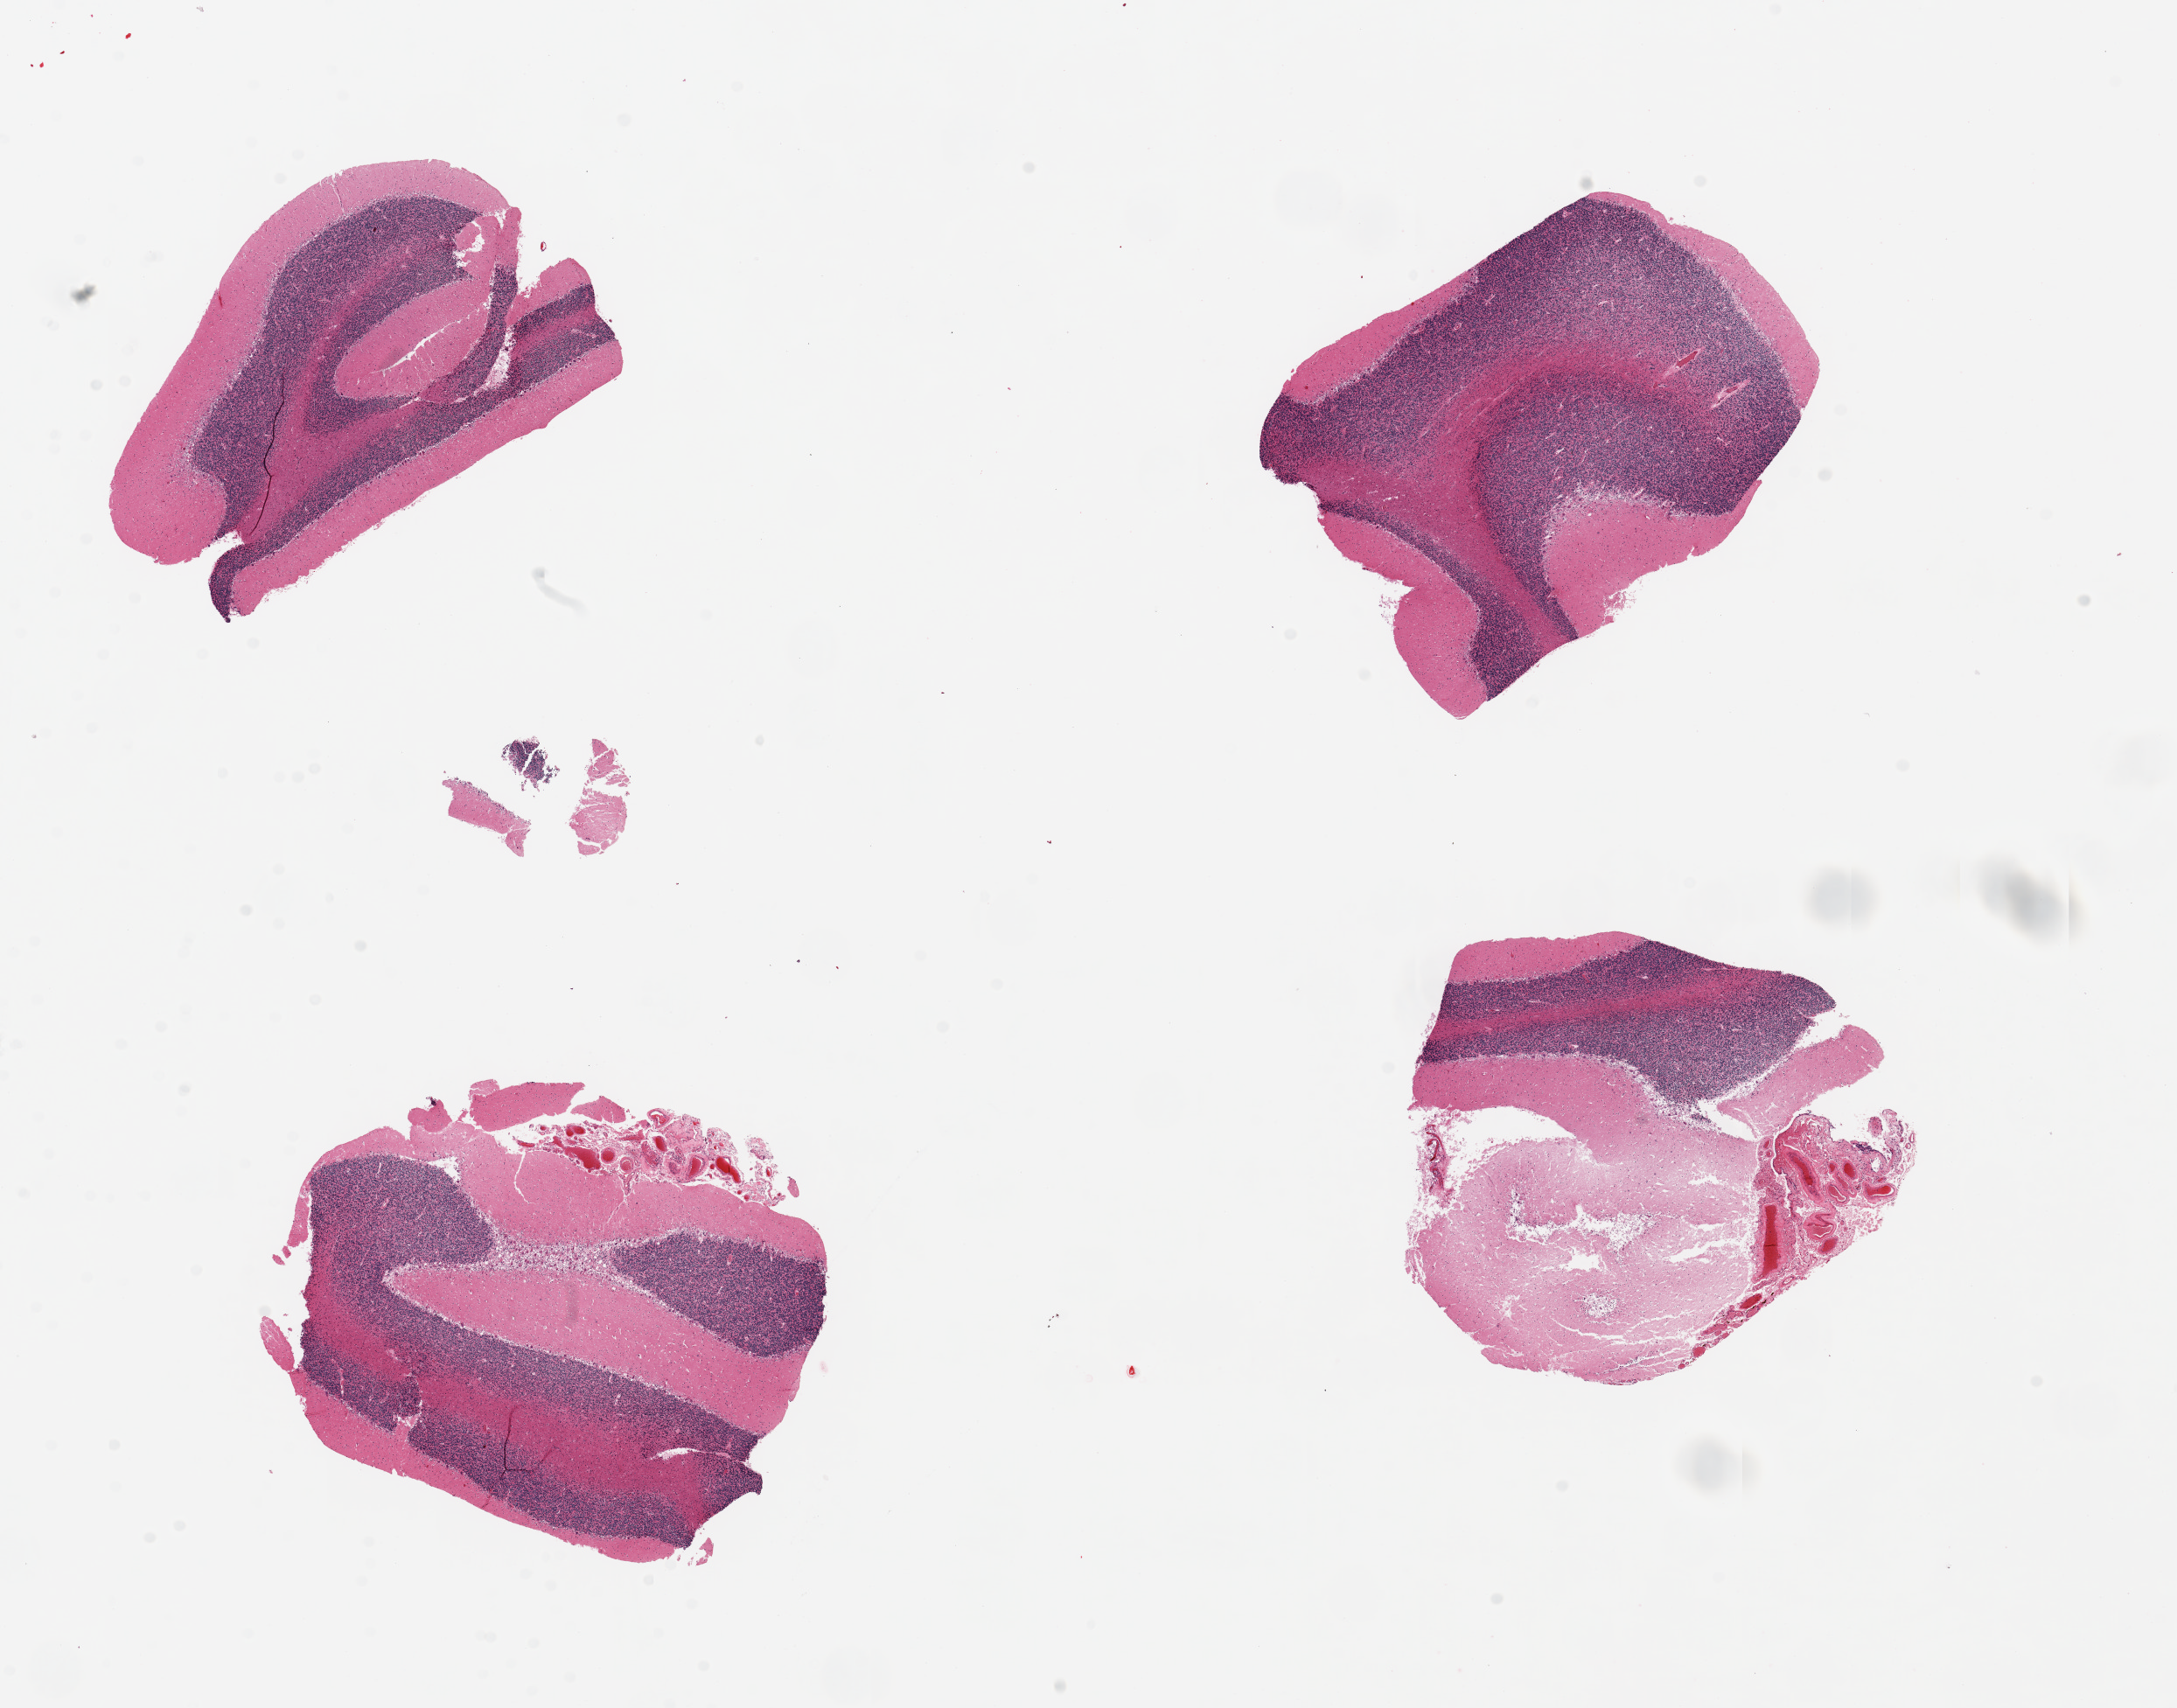
Whole-slide image, H&E stain, shown as a low-resolution overview of the whole scanned area (about 19.7 x 15.4 mm); PAXgene-fixed, paraffin-embedded tissue; section of cerebellum (target tissue); tissue donor sample. Donor: male.
- pathologist's review note for this sample: 4 pieces 4x3mm